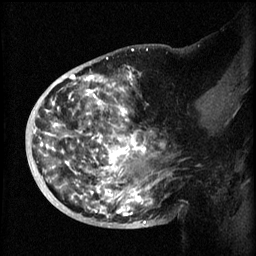
Breast MRI (dynamic contrast-enhanced), one sagittal slice; 3 images stored at this slice position (order not interpretable as contrast timing); 1.5 T; TE 4.2 ms, TR 8.2 ms; 2 mm slice thickness; 256 × 256 image matrix, field of view 200 × 200 mm. Female patient, age 50 years.
Structures marked on this image (semi-automatic segmentation, software-assisted and operator-edited):
- analysis volume of interest (the breast-tissue region the enhancement analysis was run in; not a lesion): box from (x=44, y=72) to (x=172, y=219) px
- tumour enhancement mask (voxels above the 70 % enhancement threshold inside the analysis volume of interest): (x=46, y=72)–(x=154, y=219)